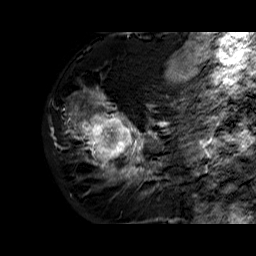
Breast MRI (dynamic contrast-enhanced), one sagittal slice; slice 21 of 60 in the series (ordered by position); dynamic contrast-enhanced series, time point 2 of 6 at this slice position (early post-contrast); 1.5 T; TE 6.3 ms, TR 32.4 ms; 4 mm slice thickness; 256 × 256 image matrix, field of view 200 × 200 mm. Female patient. Case-level facts recorded for this patient, not image findings: setting: breast cancer imaged before/during neoadjuvant chemotherapy; receptor status: HR-positive, HER2-negative.
Annotated regions visible in this slice (semi-automatically segmented with operator editing):
- analysis volume of interest (the breast-tissue region the enhancement analysis was run in; not a lesion): bounding box (x1, y1, x2, y2) in pixels: (70, 72, 177, 183)
- tumour enhancement mask (voxels above the 100 % enhancement threshold inside the analysis volume of interest): (74, 91, 166, 181)